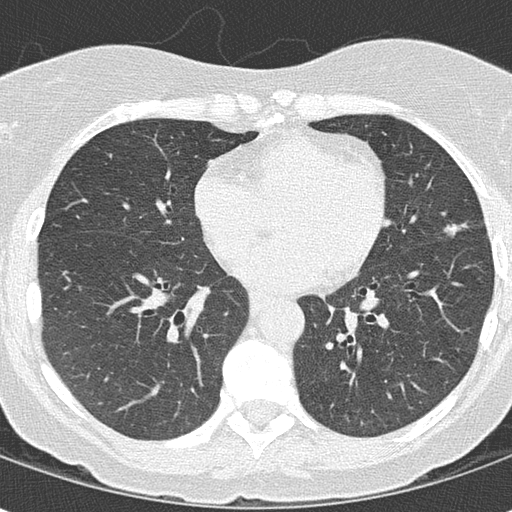
Low-dose screening chest CT, axial slice, second annual screen, lung window (W 1500 / L -600 HU), slice 79 of 163 in the series. Female participant, aged 63 years at enrolment. Current smoker at enrolment.
• Lesion marked by an expert reader, box from (x=425, y=206) to (x=479, y=255) px.
• The screening reader recorded 4 non-calcified nodules or masses ≥4 mm on this exam (right upper lobe, left lower lobe, left upper lobe, lingula); which of them this box marks is not recorded.
• Official screen result: positive, other.